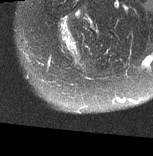
MRI of an extremity soft-tissue mass, one axial slice; position 16 of 77 along the scan axis; T2-weighted fat-saturated; MR volume resampled by the dataset authors to the PET/CT grid (not the native acquisition matrix); 3.27 mm slice thickness; 153 × 156 image matrix. Female patient. Case-level facts recorded for this patient, not image findings: histological type: synovial sarcoma; grade: intermediate; site of the primary tumour: right buttock.
Annotated regions visible in this slice (expert contour drawn on MRI and transferred to this co-registered scan by the dataset authors):
- gross tumour volume including surrounding oedema: bounding box <58,18,79,60> (left, top, right, bottom; pixels)